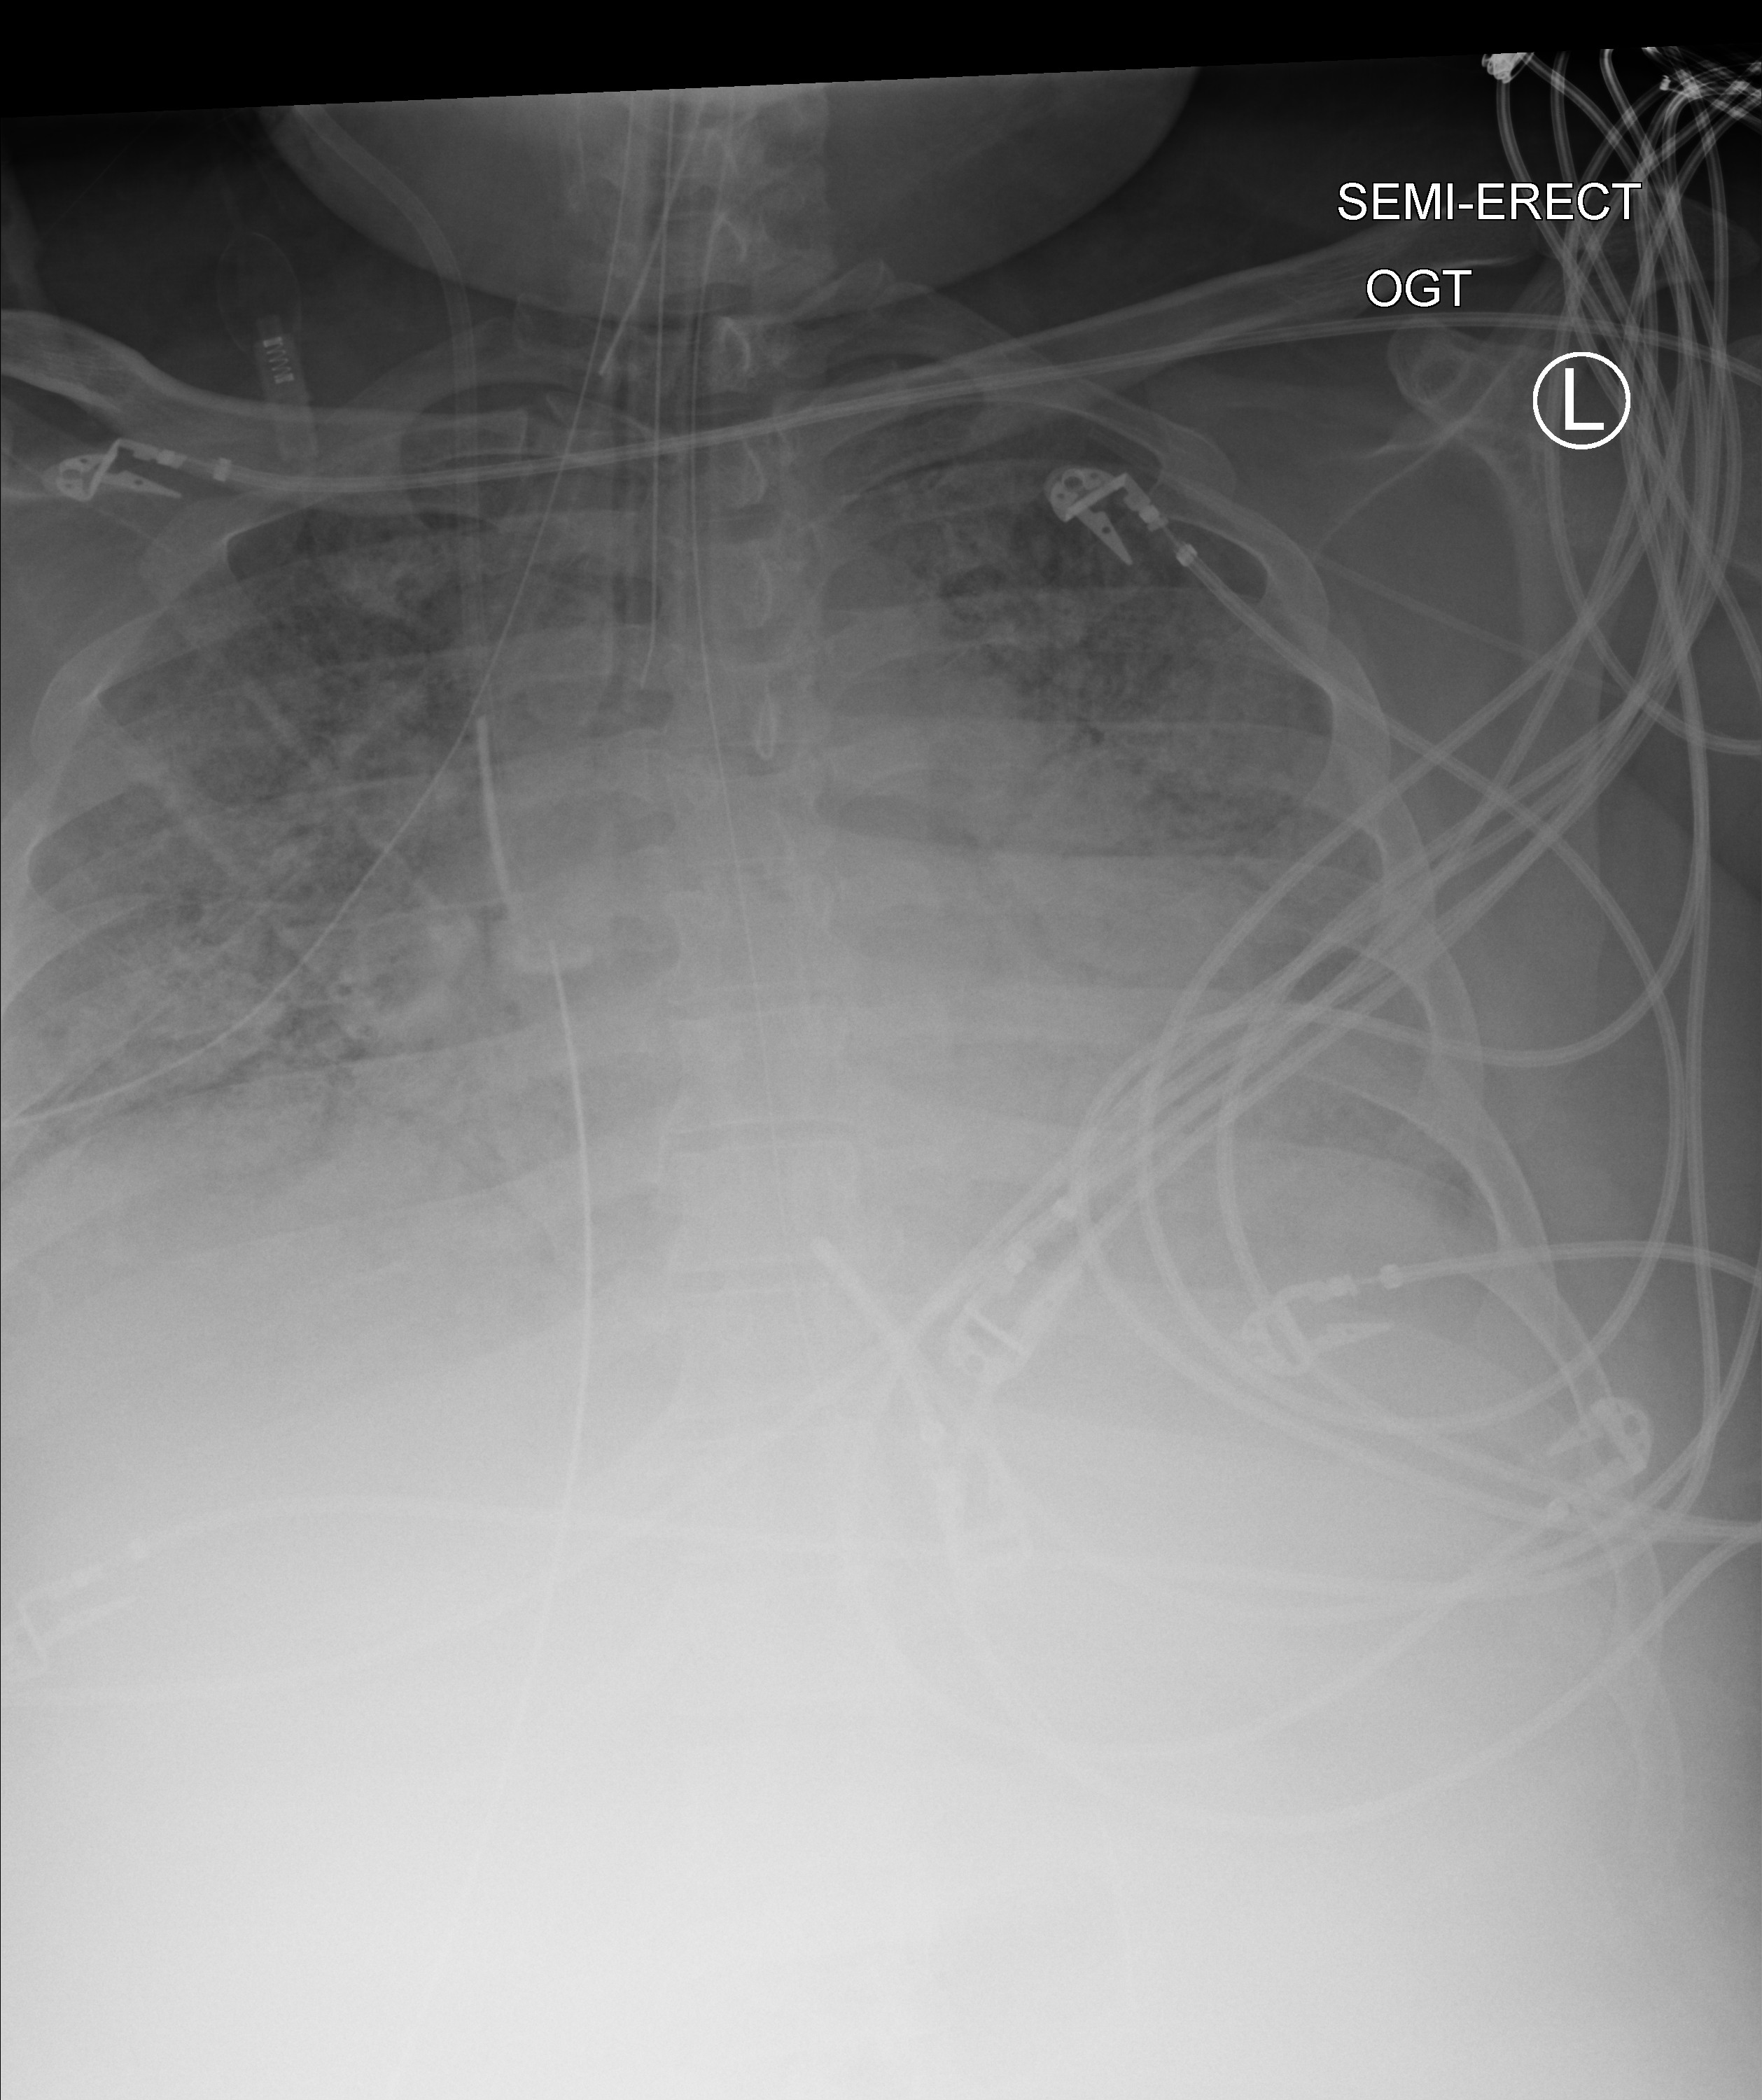
Bedside chest radiograph (computed radiography), anteroposterior (AP) projection. Adult patient hospitalised with COVID-19, age 18–59 years.
Hospital-stay facts (about this admission, not read from this image; timing relative to this image not recorded):
- admitted to intensive care during this hospital stay: yes